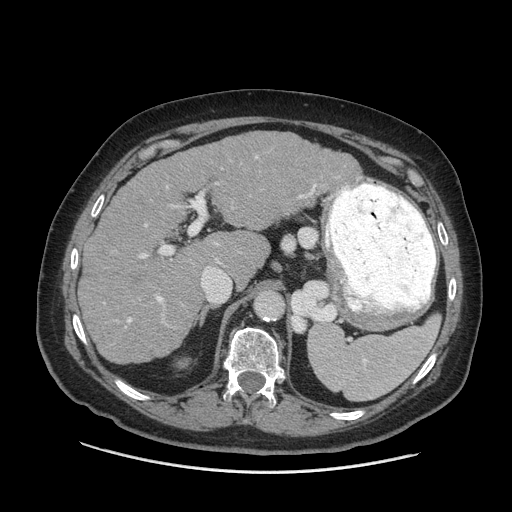
Contrast-enhanced abdominal CT (liver protocol), one axial slice. Position 42 of 77 along the scan axis. Reconstruction kernel STANDARD. 140 kVp. Soft-tissue window (W 400 / L 40 HU). 512 × 512 image matrix. Case-level facts recorded for this patient, not image findings: diagnosis: hepatocellular carcinoma (patient treated with transarterial chemoembolisation; whether this scan precedes or follows treatment is not stated here); TNM stage (as recorded): Stage-I; Child-Pugh class: A; tumour differentiation: well differentiated; tumour nodularity: uninodular.
Outlined on this slice (semi-automatically segmented with operator editing):
- liver parenchyma outside the tumour (the mass and vessels are separate outlines, so this box may not span the whole liver): box from (x=78, y=130) to (x=362, y=364) px
- liver vessels: (x=127, y=156)–(x=317, y=323)